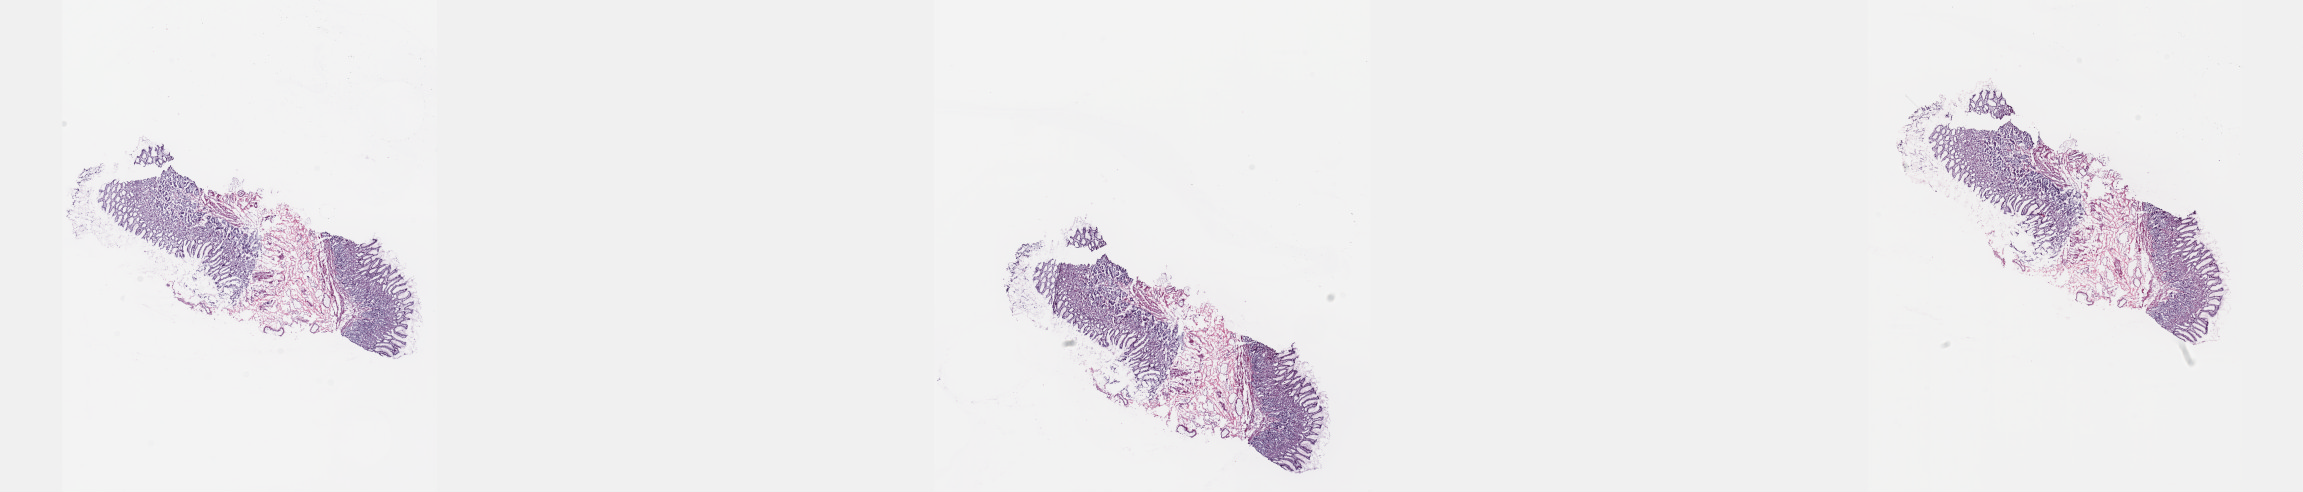
H&E whole-slide image — shown as a low-resolution overview of the whole scanned area (about 37.1 x 7.9 mm, acquisition: 20x scan), frozen section from the top of the tissue portion, esophagus, solid tissue normal (non-tumour tissue) sample. Female patient; age at initial diagnosis 71 years. Composition of this section per pathologist review: tumour cells 0%, tumour nuclei 0%, normal cells 100%, stromal cells 0%, necrosis 0%. Inflammatory infiltration, as recorded: lymphocyte infiltration 0%, monocyte infiltration 0%, neutrophil infiltration 0%.
• this section: solid tissue normal (non-tumour) sample from the same patient
• patient diagnosis: Adenocarcinoma, NOS (lower third of esophagus)